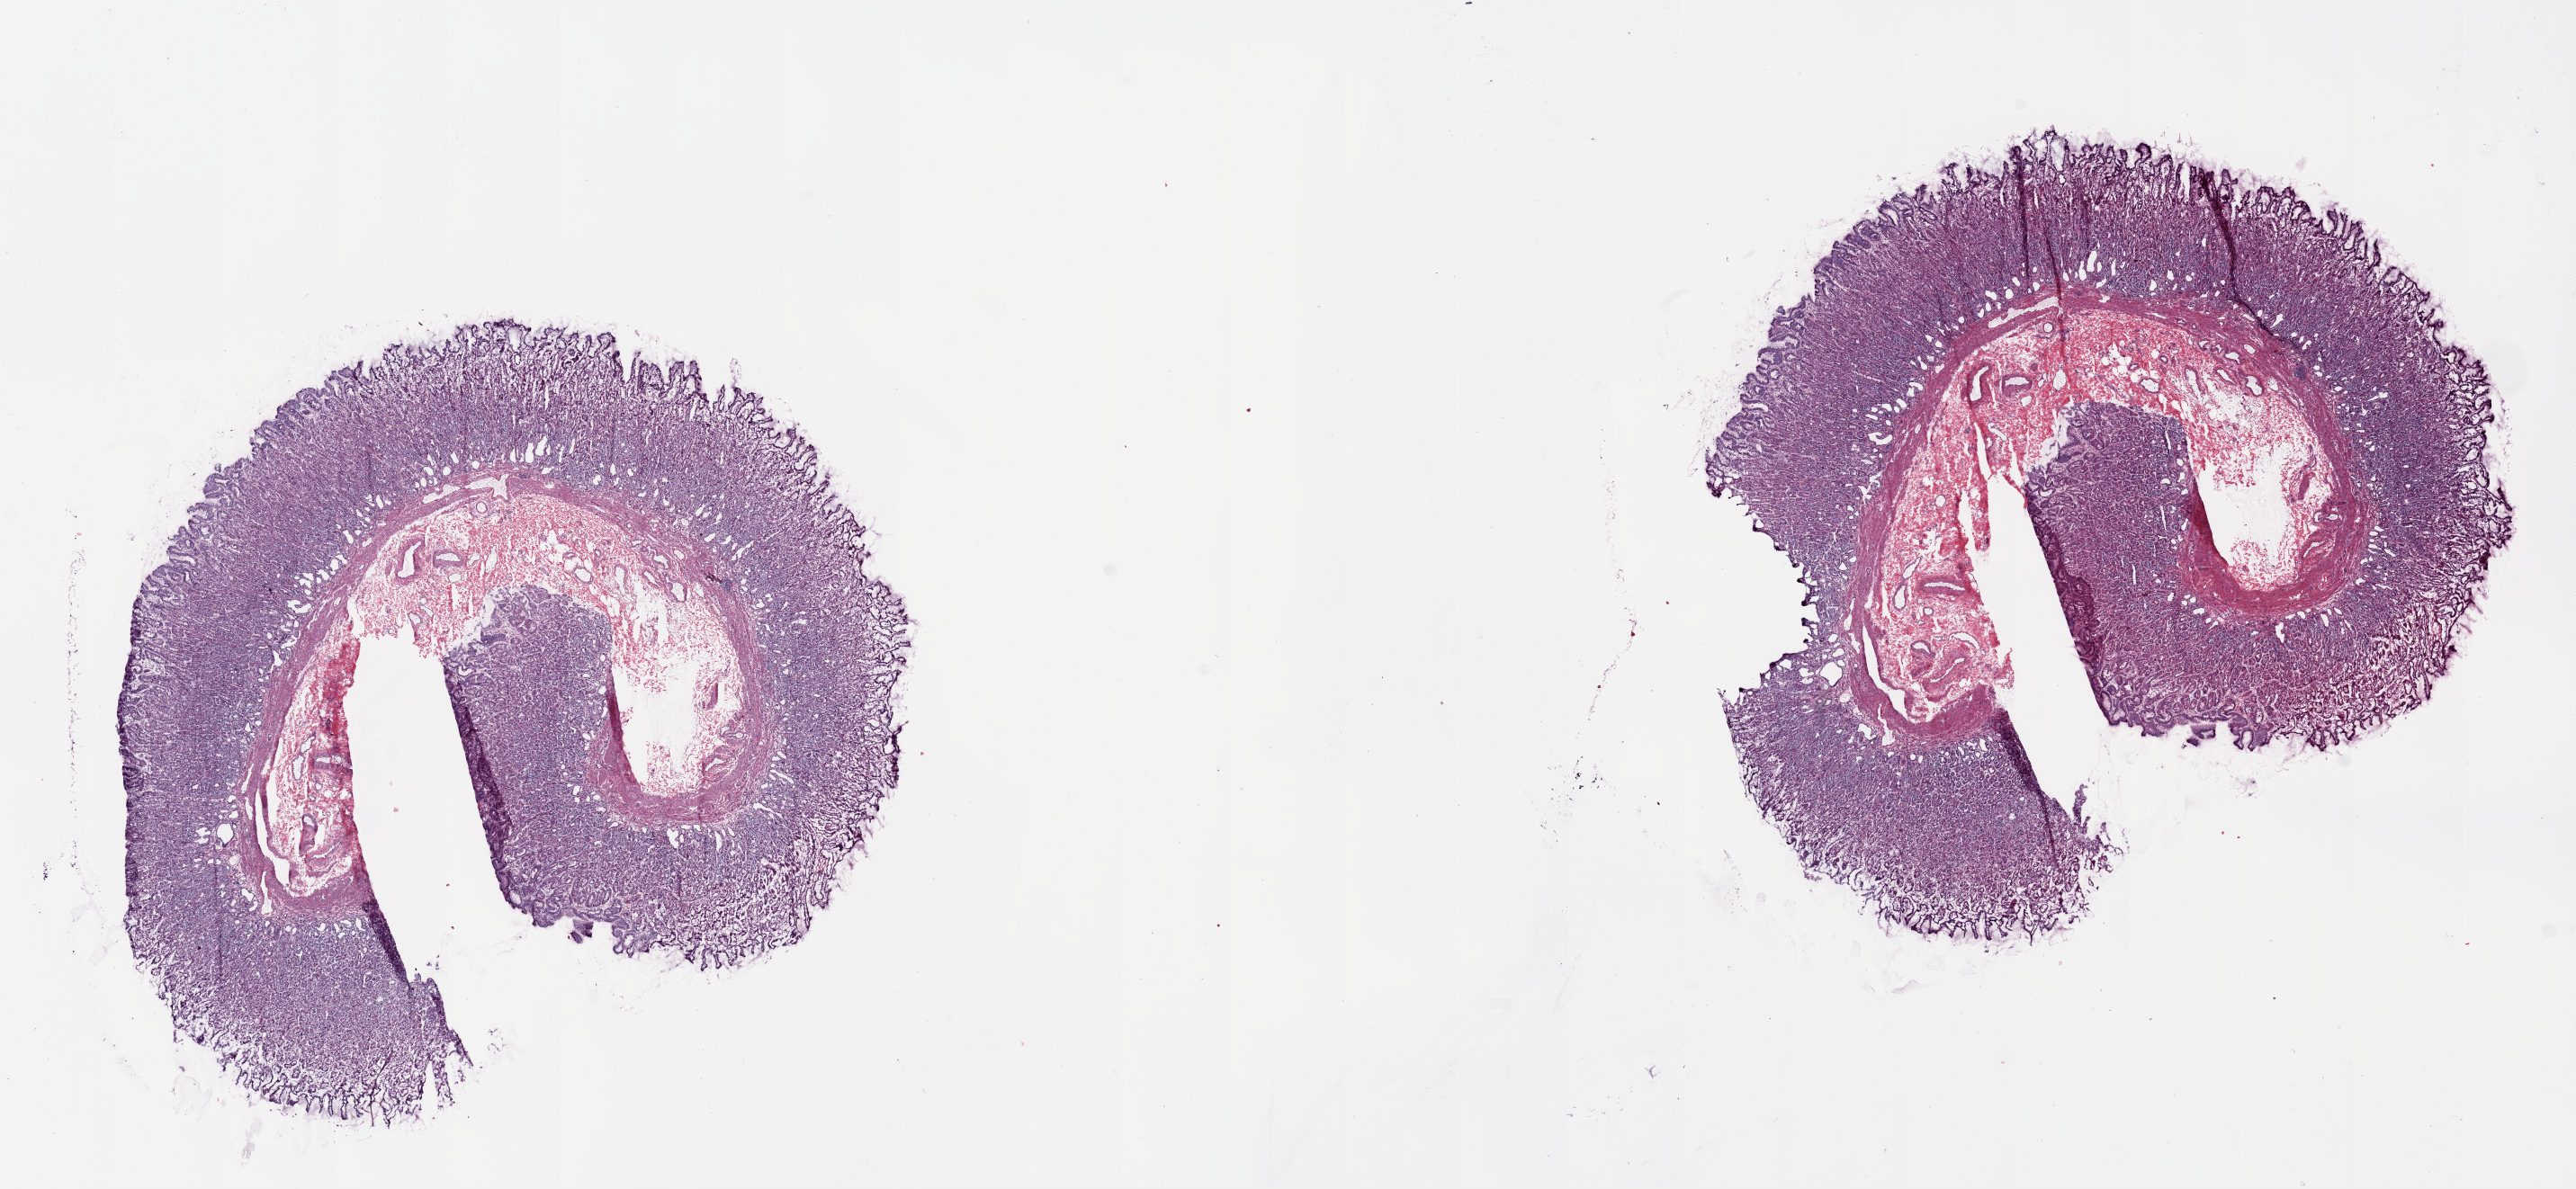
Whole-slide histology image, H&E, a low-resolution overview of the entire scanned area, about 22.6 x 10.4 mm (slide scanned at 20x). Frozen section from the top of the tissue portion. Sample: solid tissue normal (non-tumour tissue), esophagus. Patient: male, age at initial diagnosis 63 years. Composition of this section per pathologist review: tumour cells 0%, tumour nuclei 0%, normal cells 70%, stromal cells 30%, necrosis 0%. Inflammatory infiltration, as recorded: lymphocyte infiltration 10%, monocyte infiltration 0%, neutrophil infiltration 0%.
* this section: solid tissue normal (non-tumour) sample from the same patient
* patient diagnosis: Adenocarcinoma, NOS (lower third of esophagus)